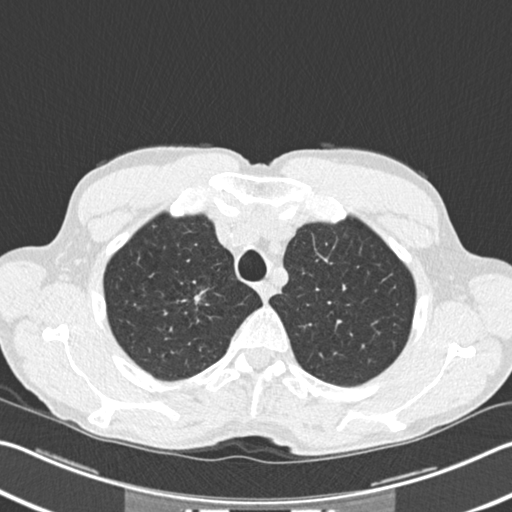
Low-dose screening chest CT, one axial slice. Position 185 of 220 along the scan axis. Reconstruction kernel B30f. 120 kVp. Lung window (W 1500 / L -600 HU). 512 × 512 image matrix, field of view 342 × 342 mm.
Structures marked on this image (outlined manually by an expert reader):
- lesion 1 (tumor, upper lobe of right lung): bounding box [x1, y1, x2, y2] px = [194, 295, 201, 303]